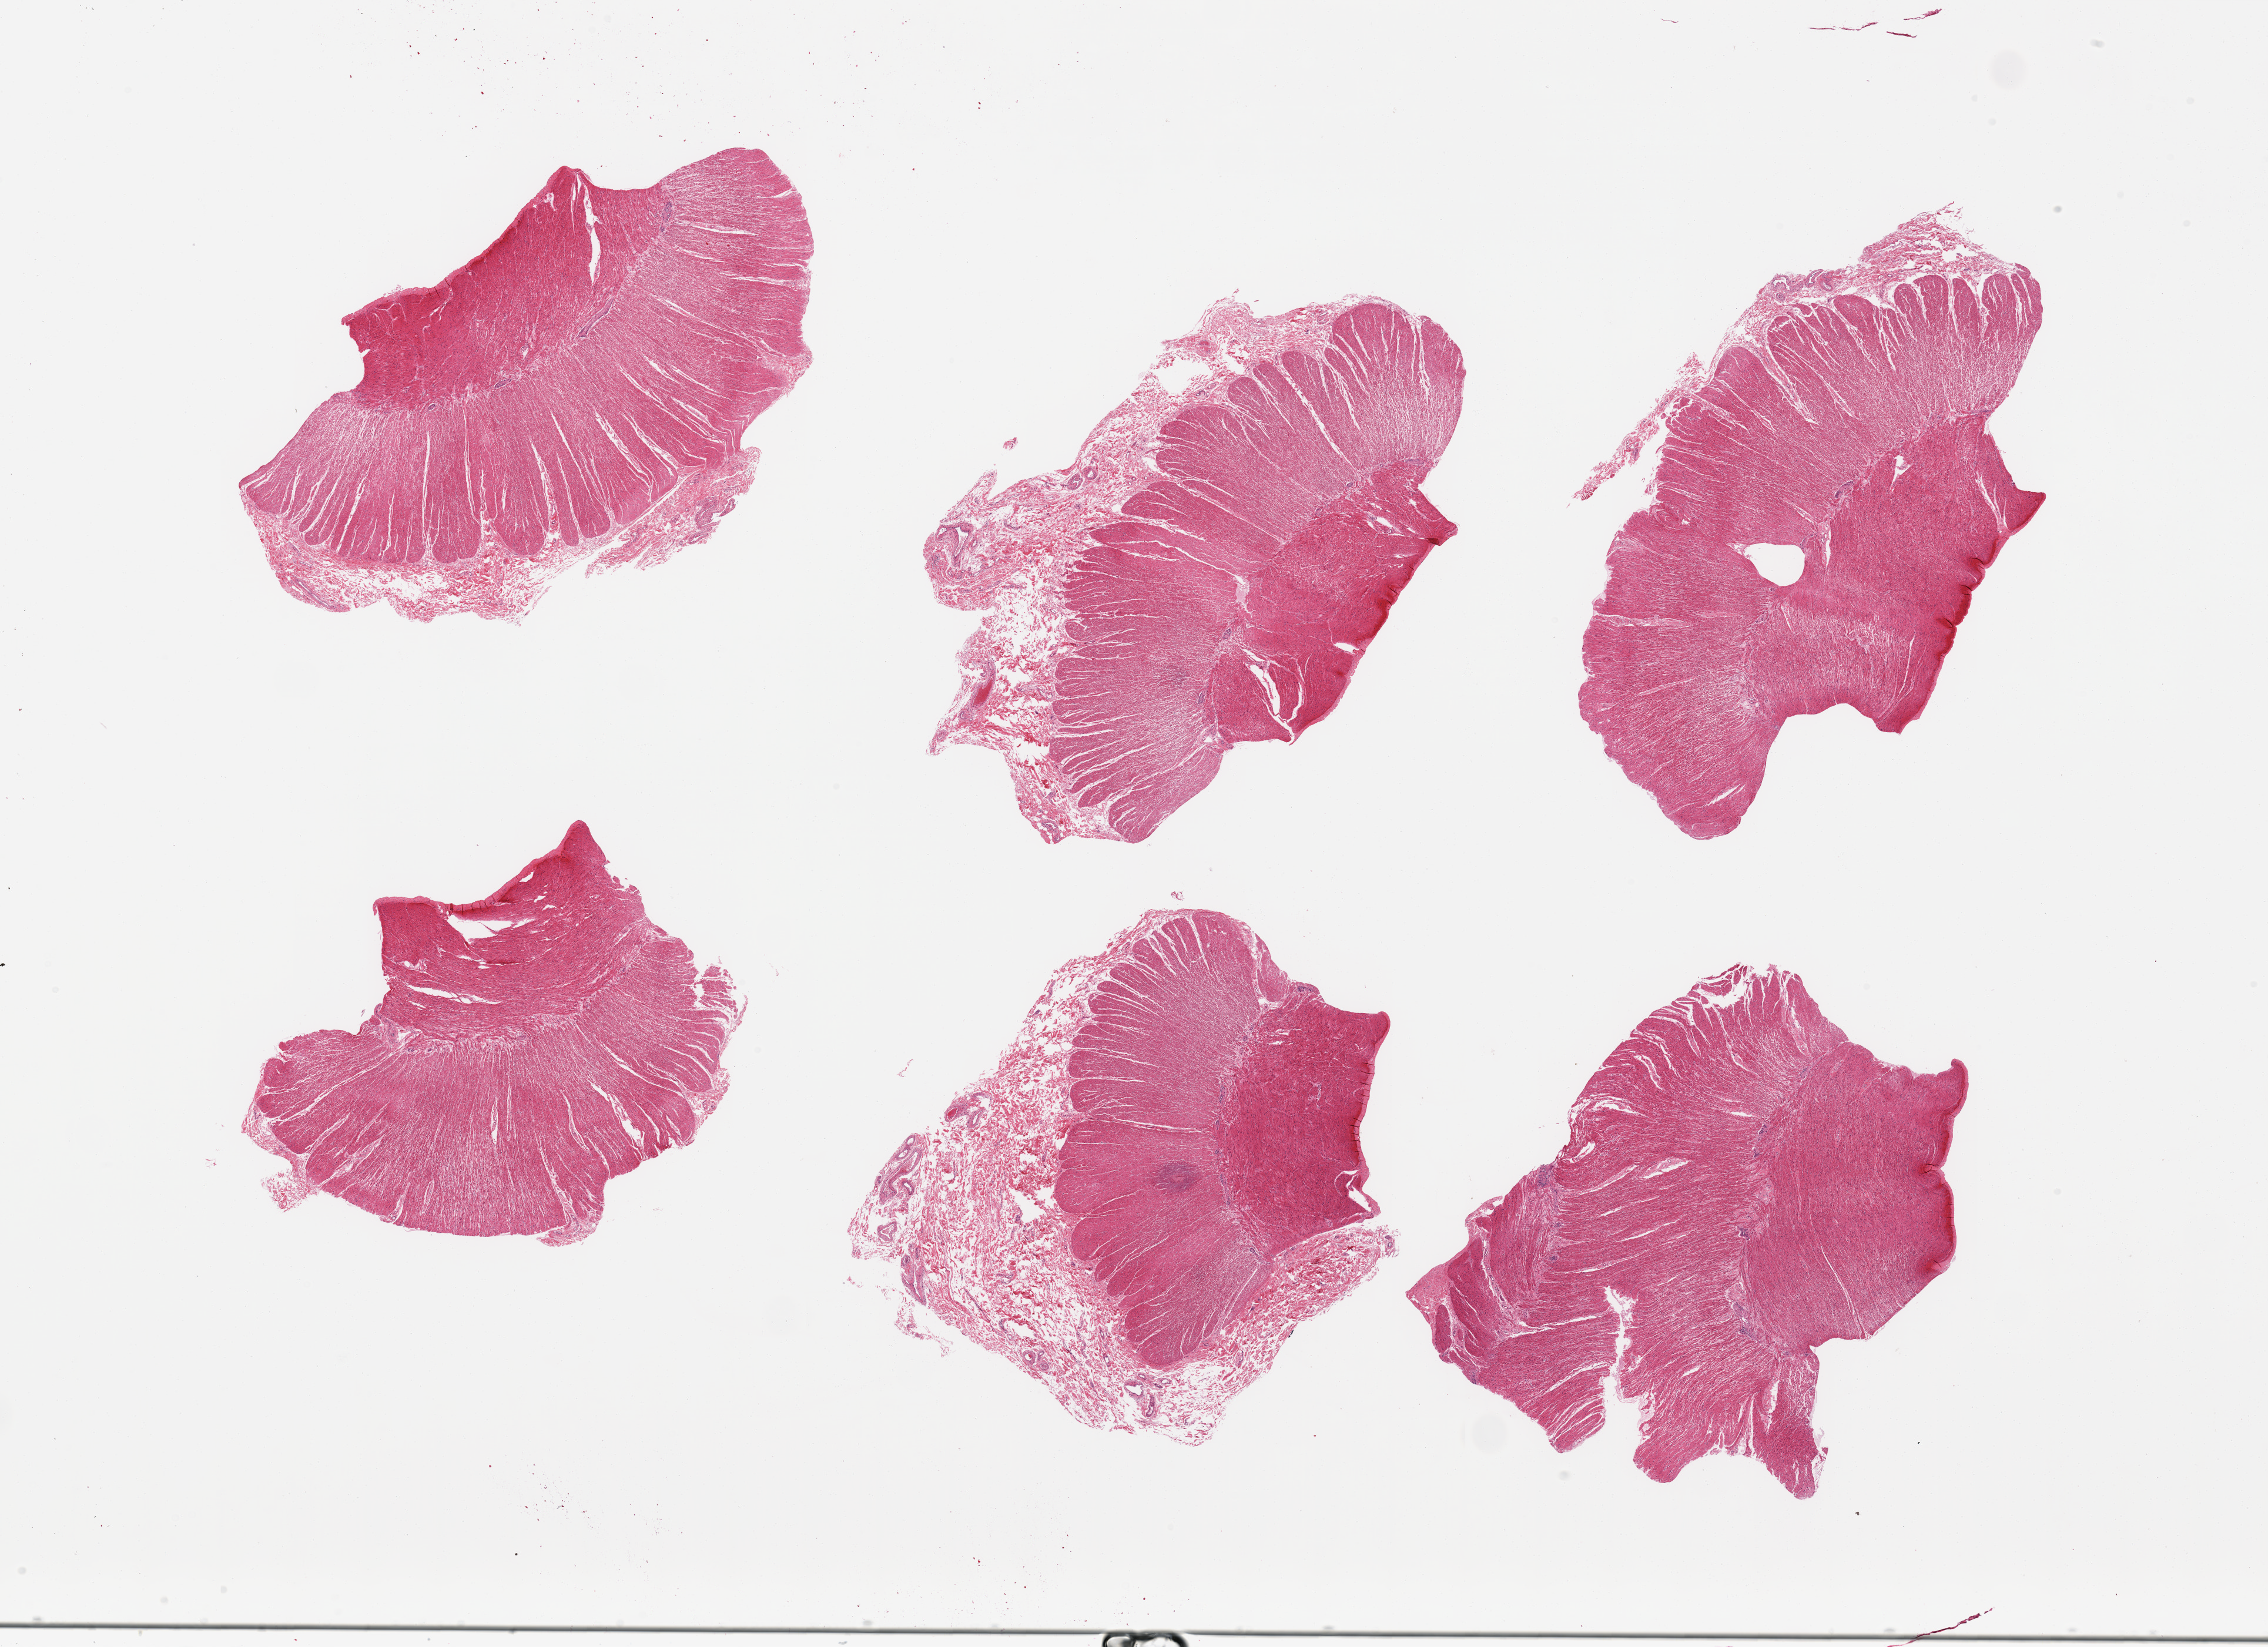
Hematoxylin and eosin (H&E) whole-slide image, shown as a low-resolution overview of the whole scanned area (about 30.5 x 22.2 mm, acquisition: 20x scan); PAXgene-fixed, paraffin-embedded tissue; sampled site (target tissue): sigmoid colon; donor tissue sample. Male donor.
Pathologist's review note for this sample: 6 pieces, confirmed target muscularis.